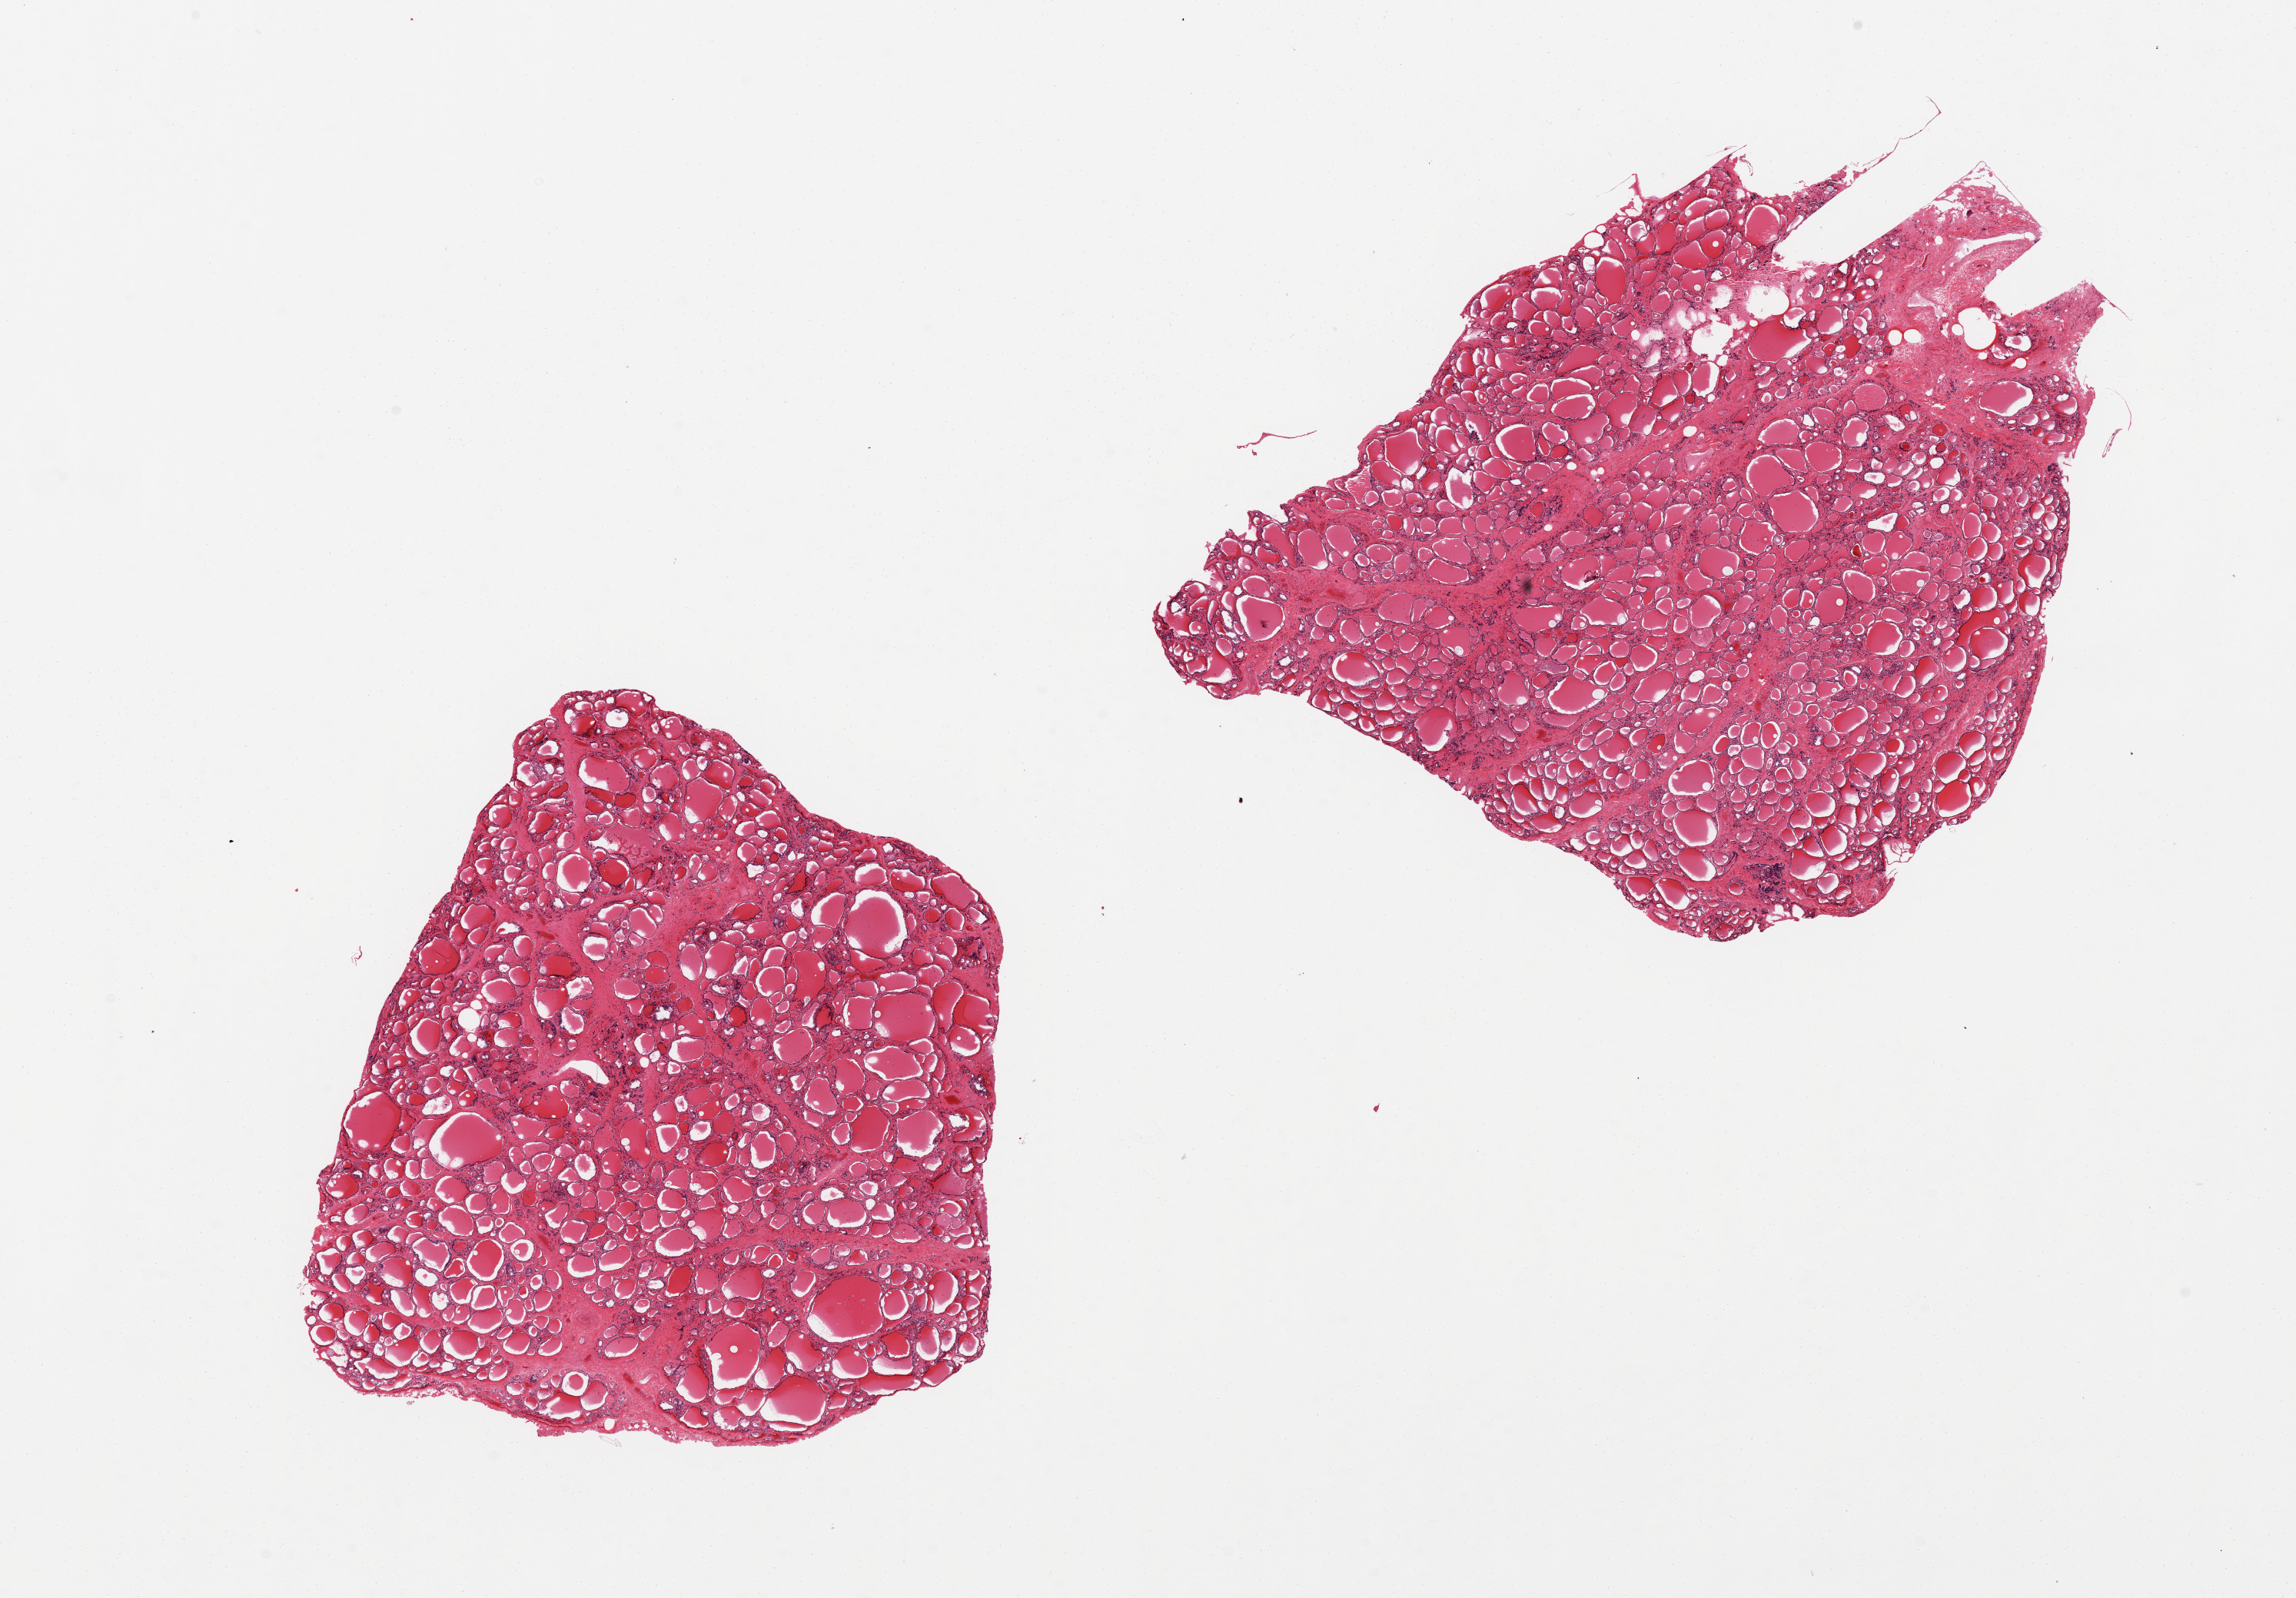
Digitized haematoxylin and eosin-stained section, brightfield — a low-resolution overview of the entire scanned area, about 23.6 x 16.4 mm, PAXgene-fixed paraffin-embedded (PFPE) section, sampled site (target tissue): thyroid, tissue donor sample.
- pathologist's review note for this sample: 2 pieces, moderately autolyzed